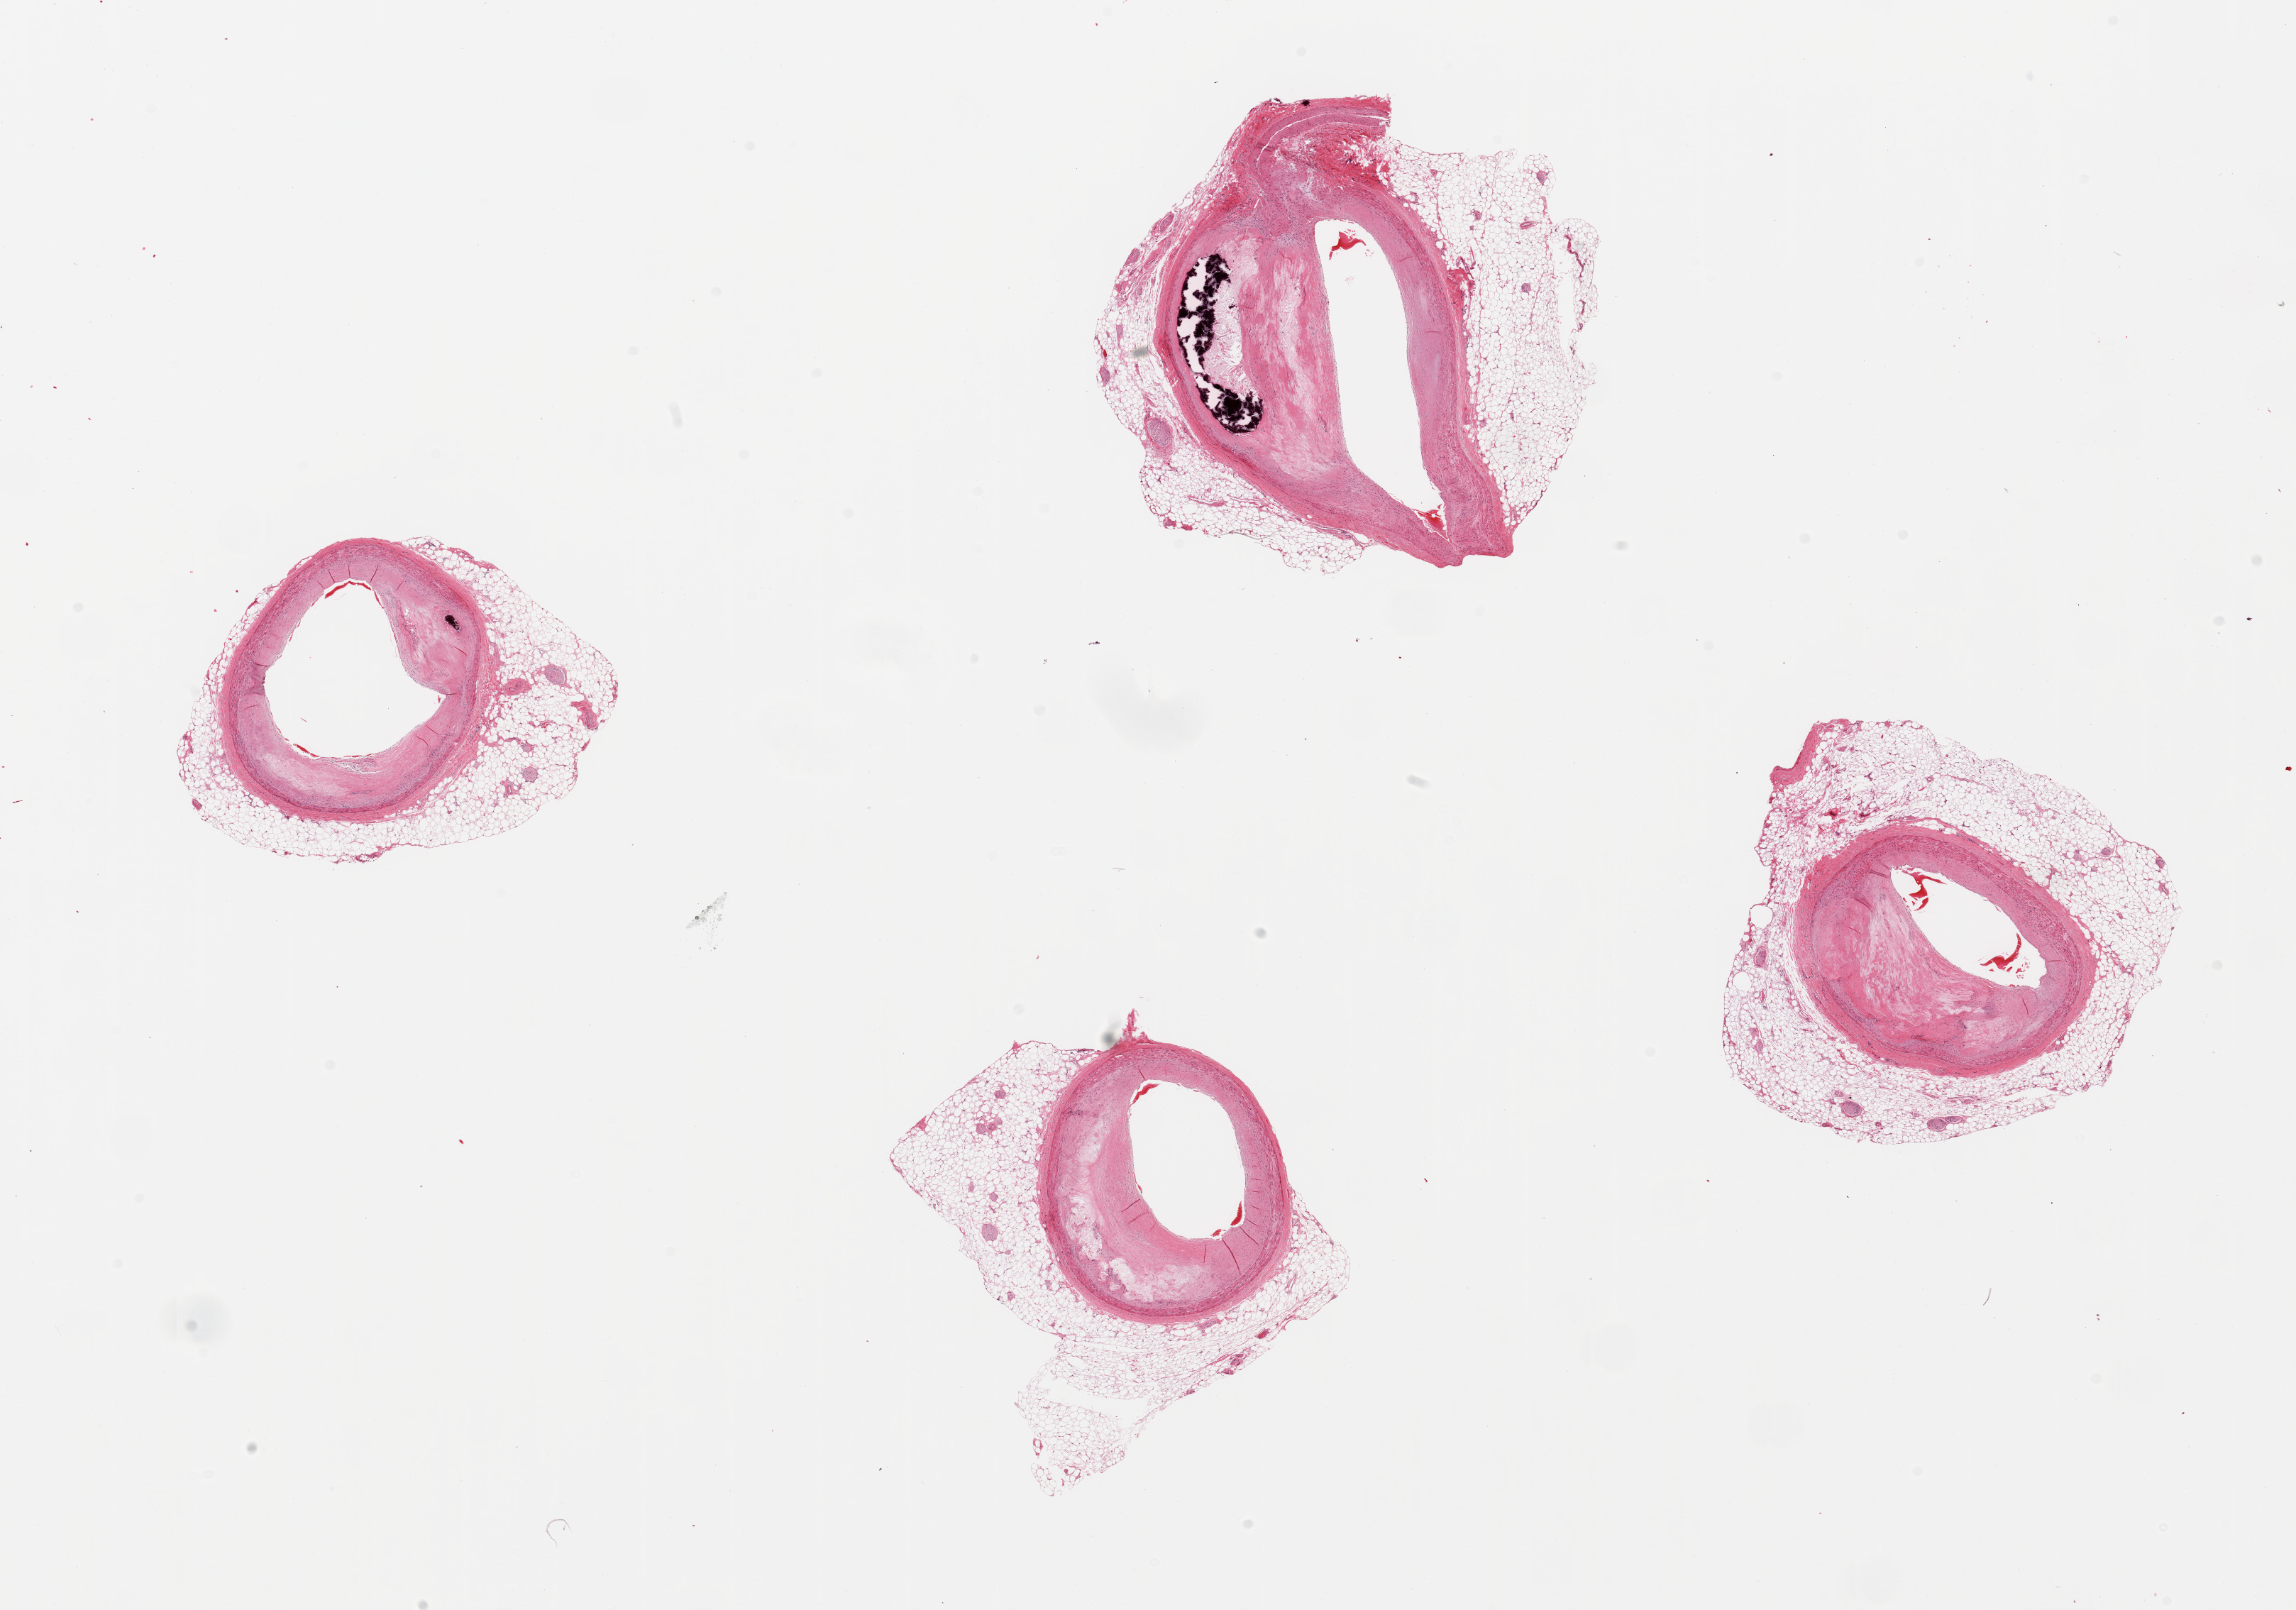
Whole-slide image, H&E stain, brightfield, low-resolution overview of the scanned area, about 25.6 x 17.9 mm (slide scanned at 20x); PAXgene-fixed, paraffin-embedded tissue; sampled site (target tissue): coronary artery; tissue donor sample. Donor: male.
Pathologist's review note for this sample: 4 pieces; eccentric atheromatous plaques narrowing up to 75% of lumen; 1 has large calcified deposit; all have extraneous external fat up to 1.6 mm thick.